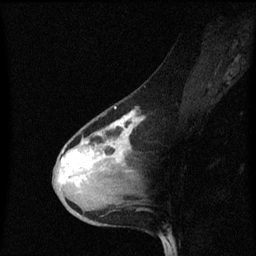
Breast MRI (dynamic contrast-enhanced), one sagittal slice. Position 38 of 60 along the scan axis. Dynamic contrast-enhanced series, image 2 of 3 at this slice position (ordered by acquisition). 1.5 T. TE 4.2 ms, TR 8.4 ms. 2 mm slice thickness. 256 × 256 image matrix, field of view 200 × 200 mm. Female patient, age 38 years. Case-level facts recorded for this patient, not image findings: setting: breast cancer imaged before/during neoadjuvant chemotherapy; receptor status: HR-positive, HER2-negative.
Structures marked on this image (semi-automatically segmented with operator editing):
- analysis volume of interest (the breast-tissue region the enhancement analysis was run in; not a lesion): bounding box <54,102,141,205> (left, top, right, bottom; pixels)
- tumour enhancement mask (voxels above the 70 % enhancement threshold inside the analysis volume of interest): <60,110,141,181>